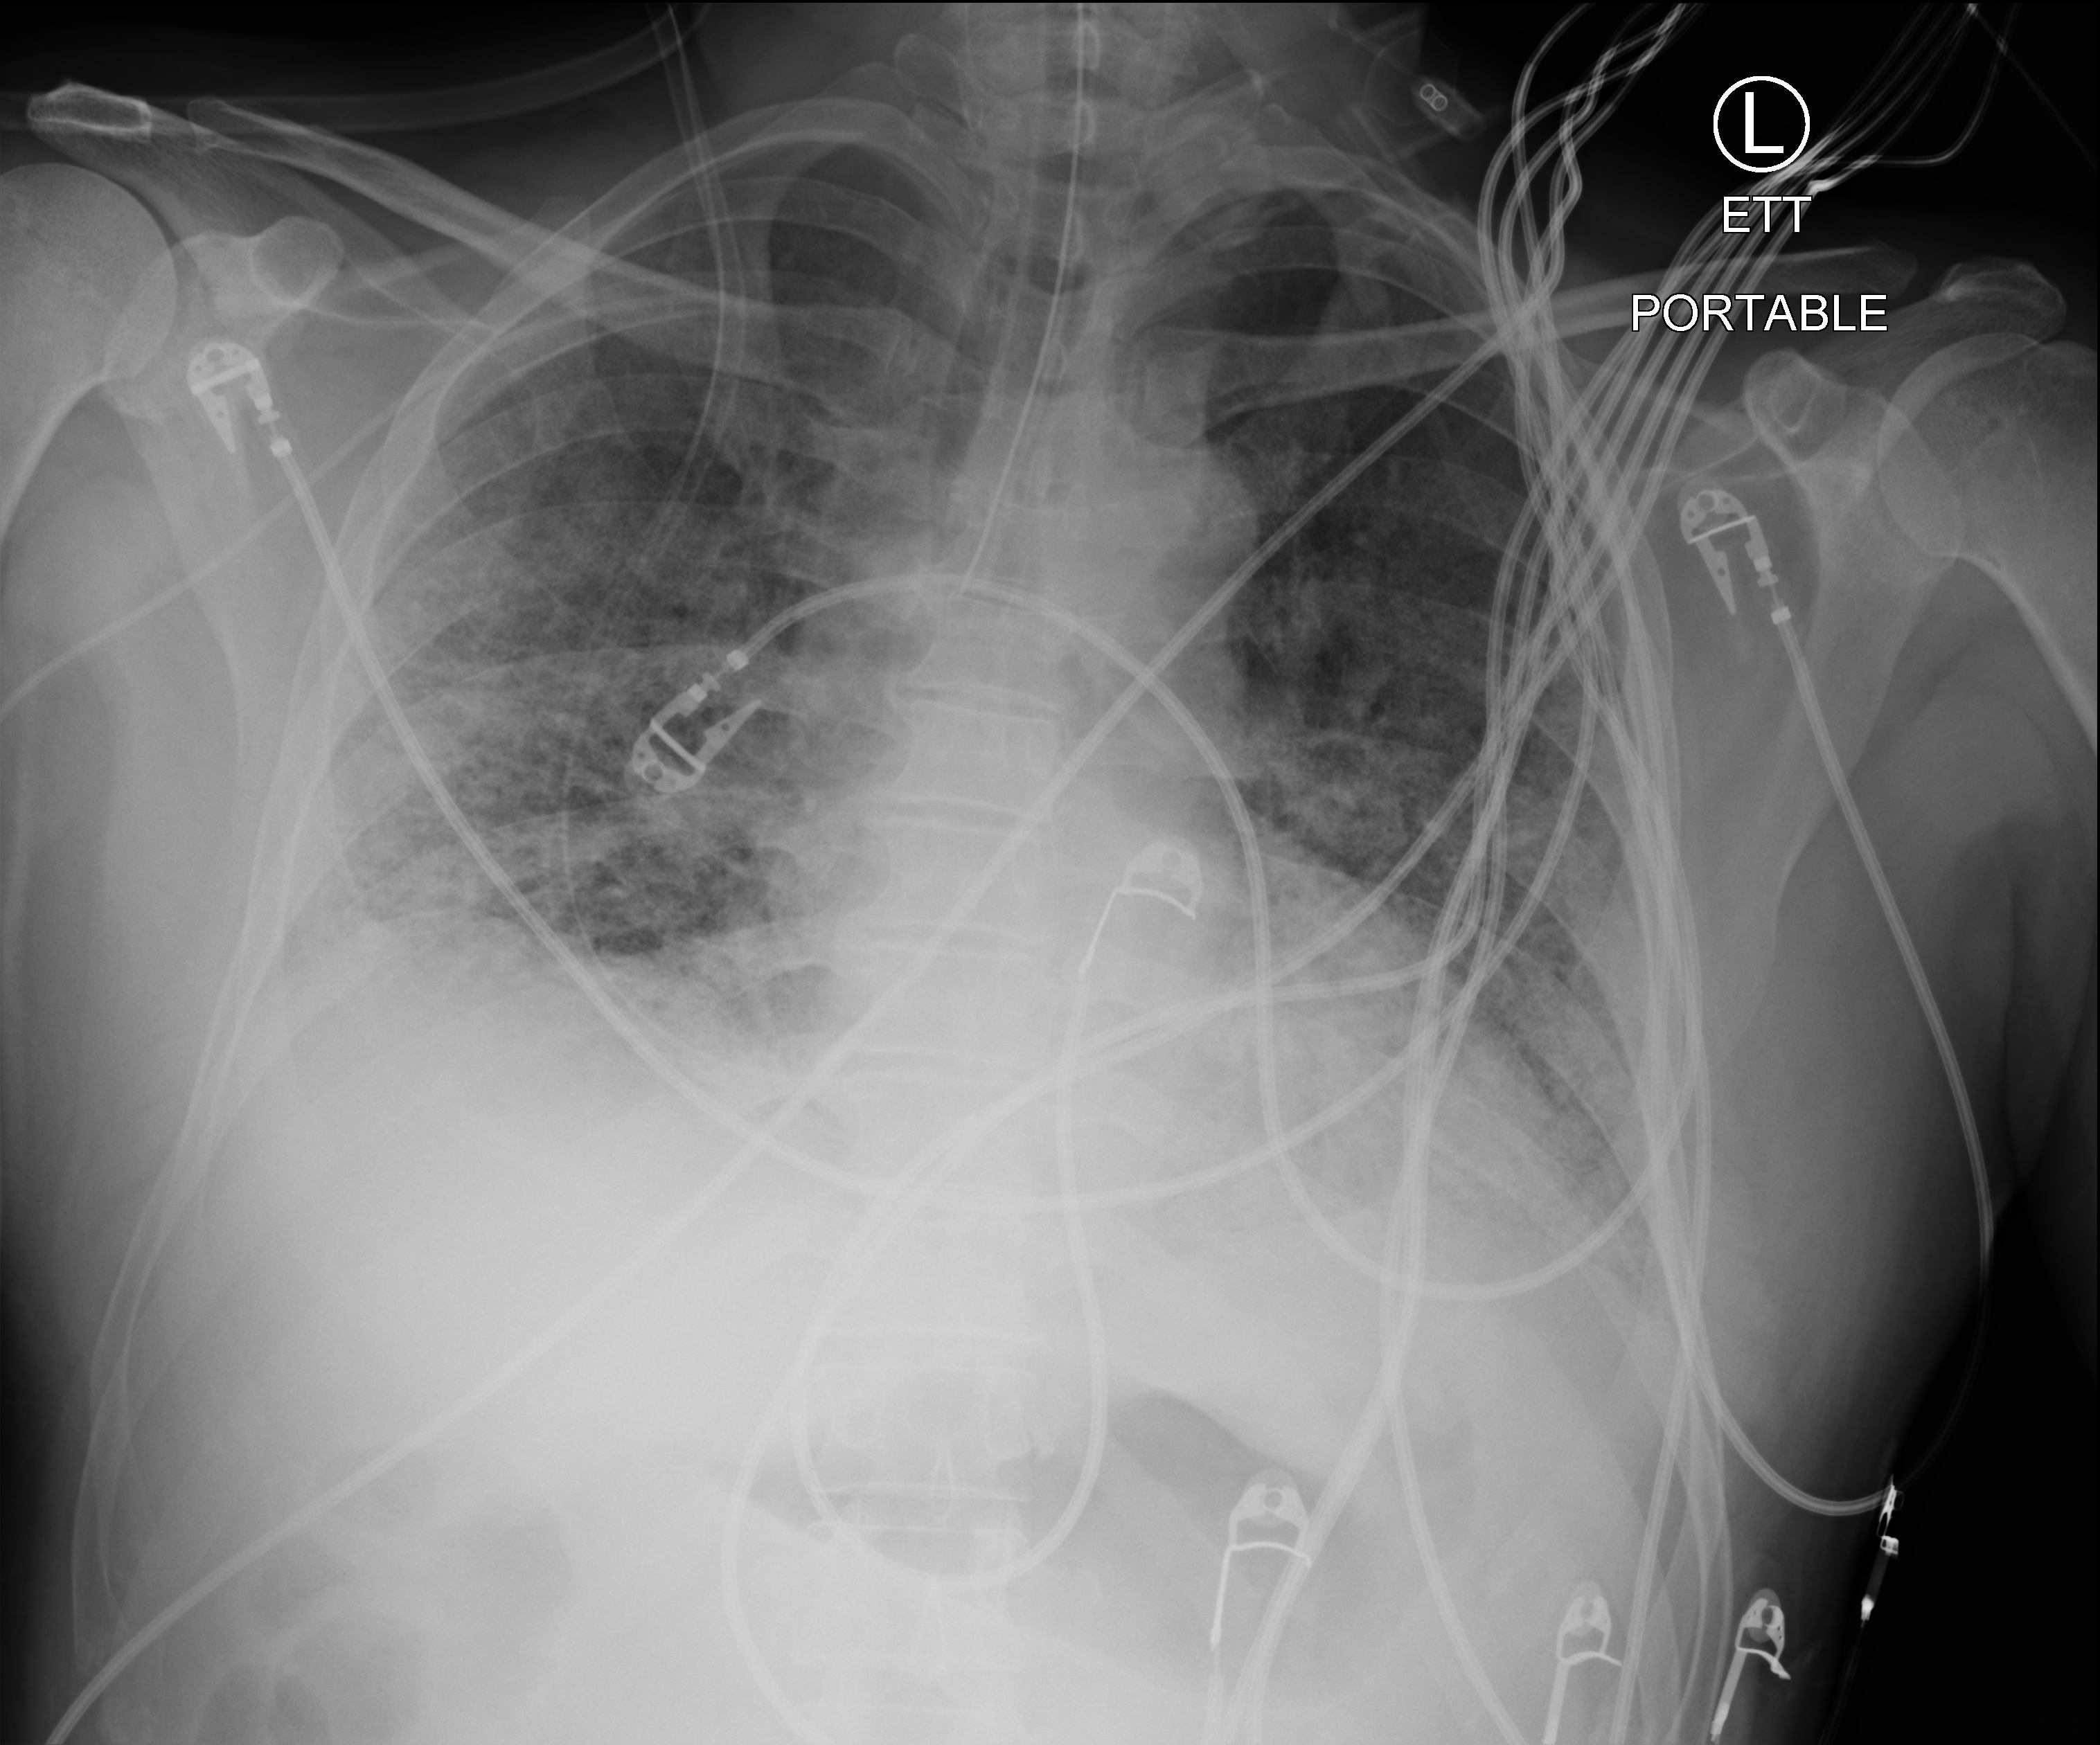
Chest X-ray (portable); anteroposterior (AP) projection. Male patient hospitalised with COVID-19, age 18–59 years.
Admission-level facts for this patient (not findings on this image; timing relative to this image not recorded): length of hospital stay: 42 days; other chronic lung disease (admission record): no; diabetes (admission record): no.